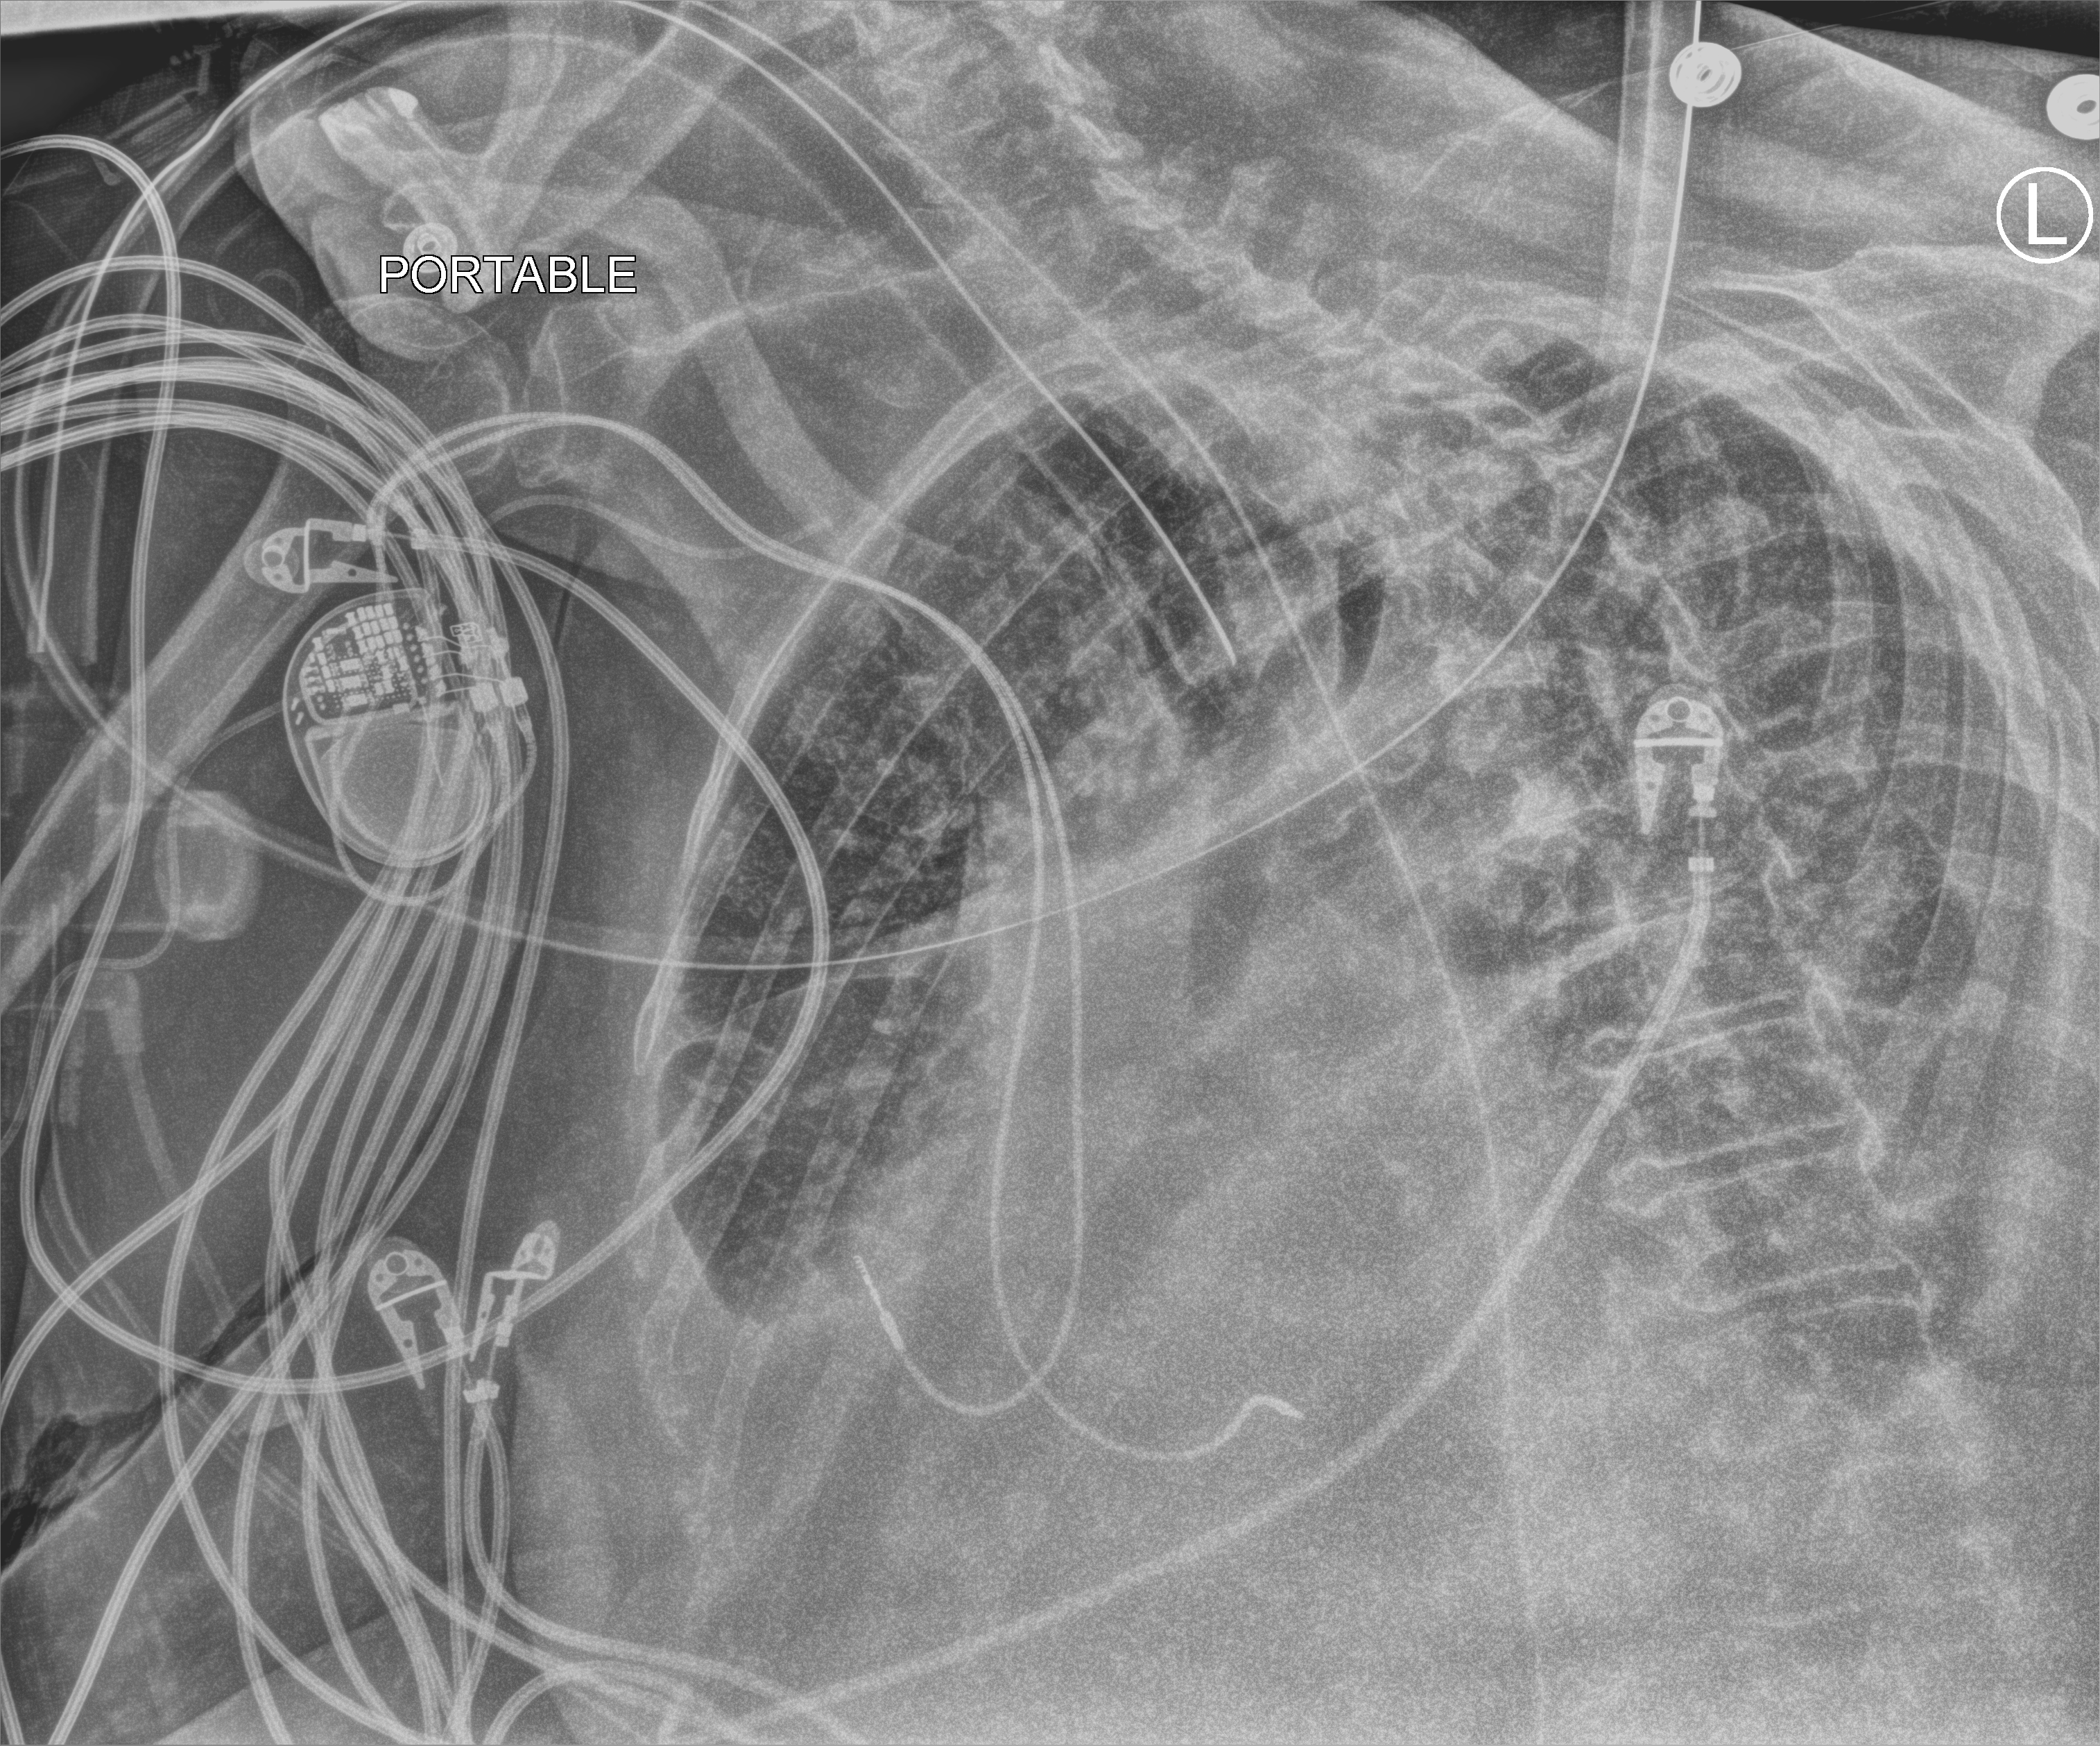
Portable chest radiograph; anteroposterior (AP) projection. Patient hospitalised with COVID-19; female, aged 75–90 years.
Hospital-stay facts (about this admission, not read from this image; timing relative to this image not recorded): admitted to intensive care during this hospital stay: yes; hypertension (admission record): yes; length of hospital stay: 21 days.